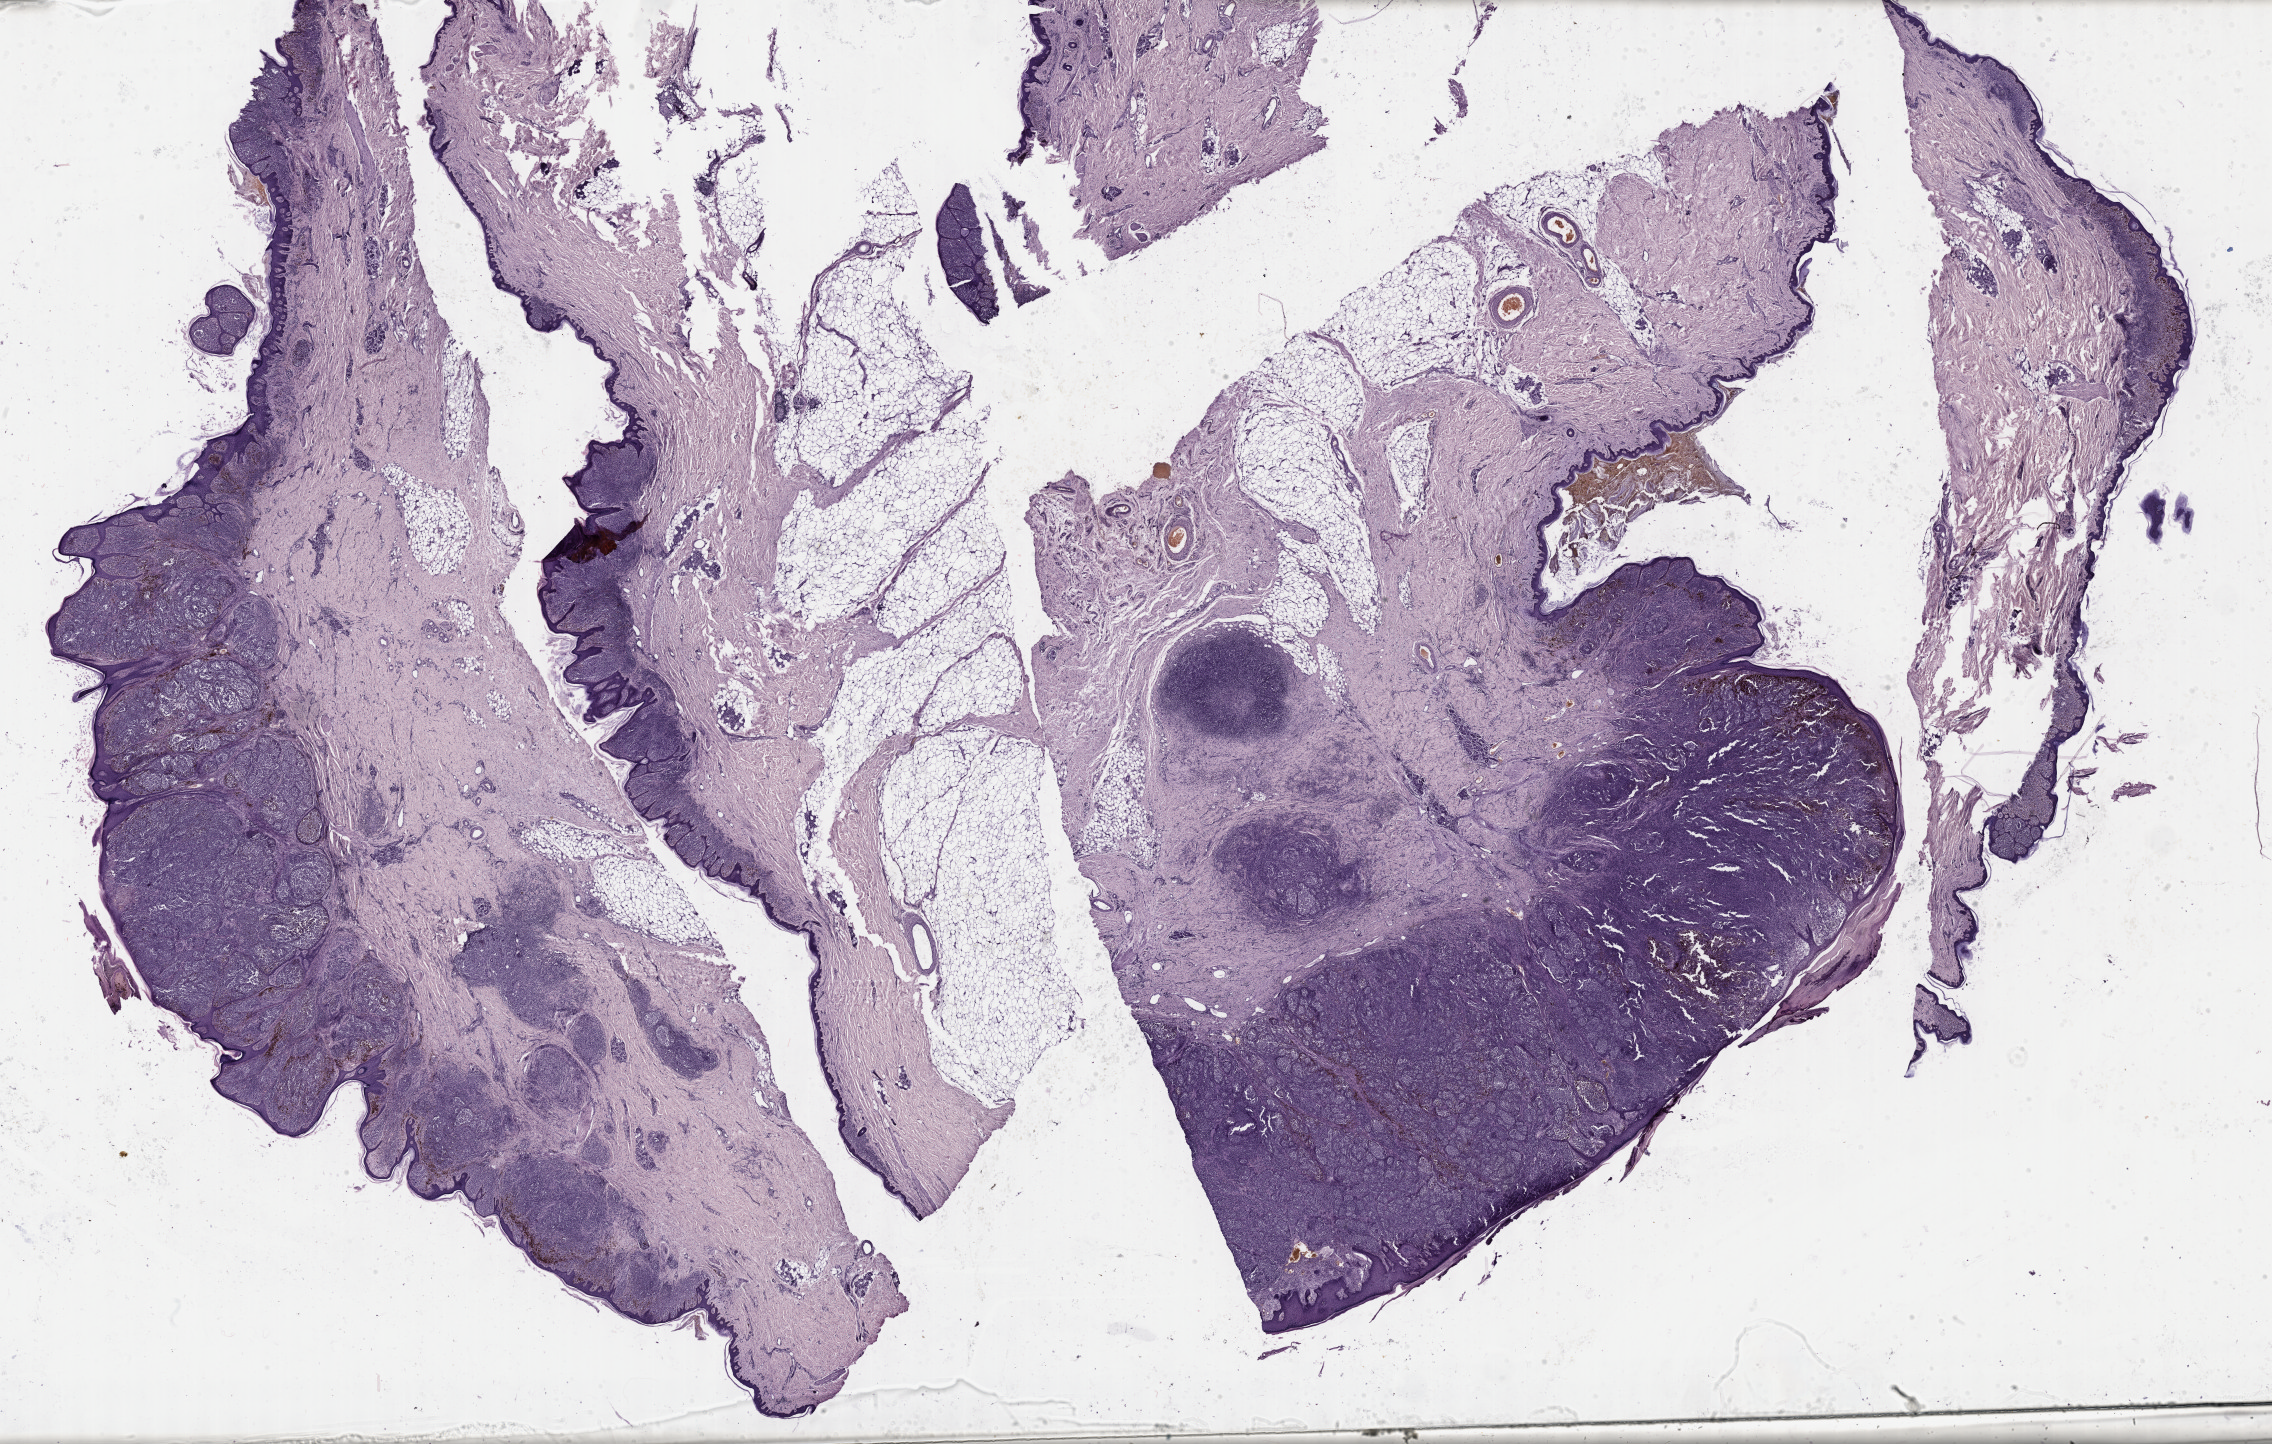
Digitized H&E-stained tissue section (whole slide), shown as a low-resolution overview of the whole scanned area (about 36.7 x 23.4 mm, slide scanned at 40x), formalin-fixed paraffin-embedded (FFPE) diagnostic section, primary tumour sample from the skin. Female, age 62 years at initial diagnosis.
* pathologic diagnosis: Malignant melanoma, NOS
* TNM: T4 N0 M0
* AJCC pathologic stage: II (7th edition)